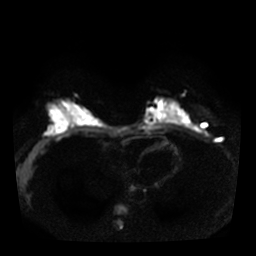
Breast MRI, one axial slice; slice 15 of 35 in the series (ordered by position); diffusion-weighted series; image 2 of 4 stored at this slice position (different b-values; order by instance number); 3 T; 5 mm slice thickness; 256 × 256 image matrix, field of view 320 × 320 mm. Female patient.
Outlined on this slice (manually delineated by an expert):
- tumour on diffusion-weighted imaging: bounding box (x1, y1, x2, y2) in pixels: (181, 109, 188, 121)